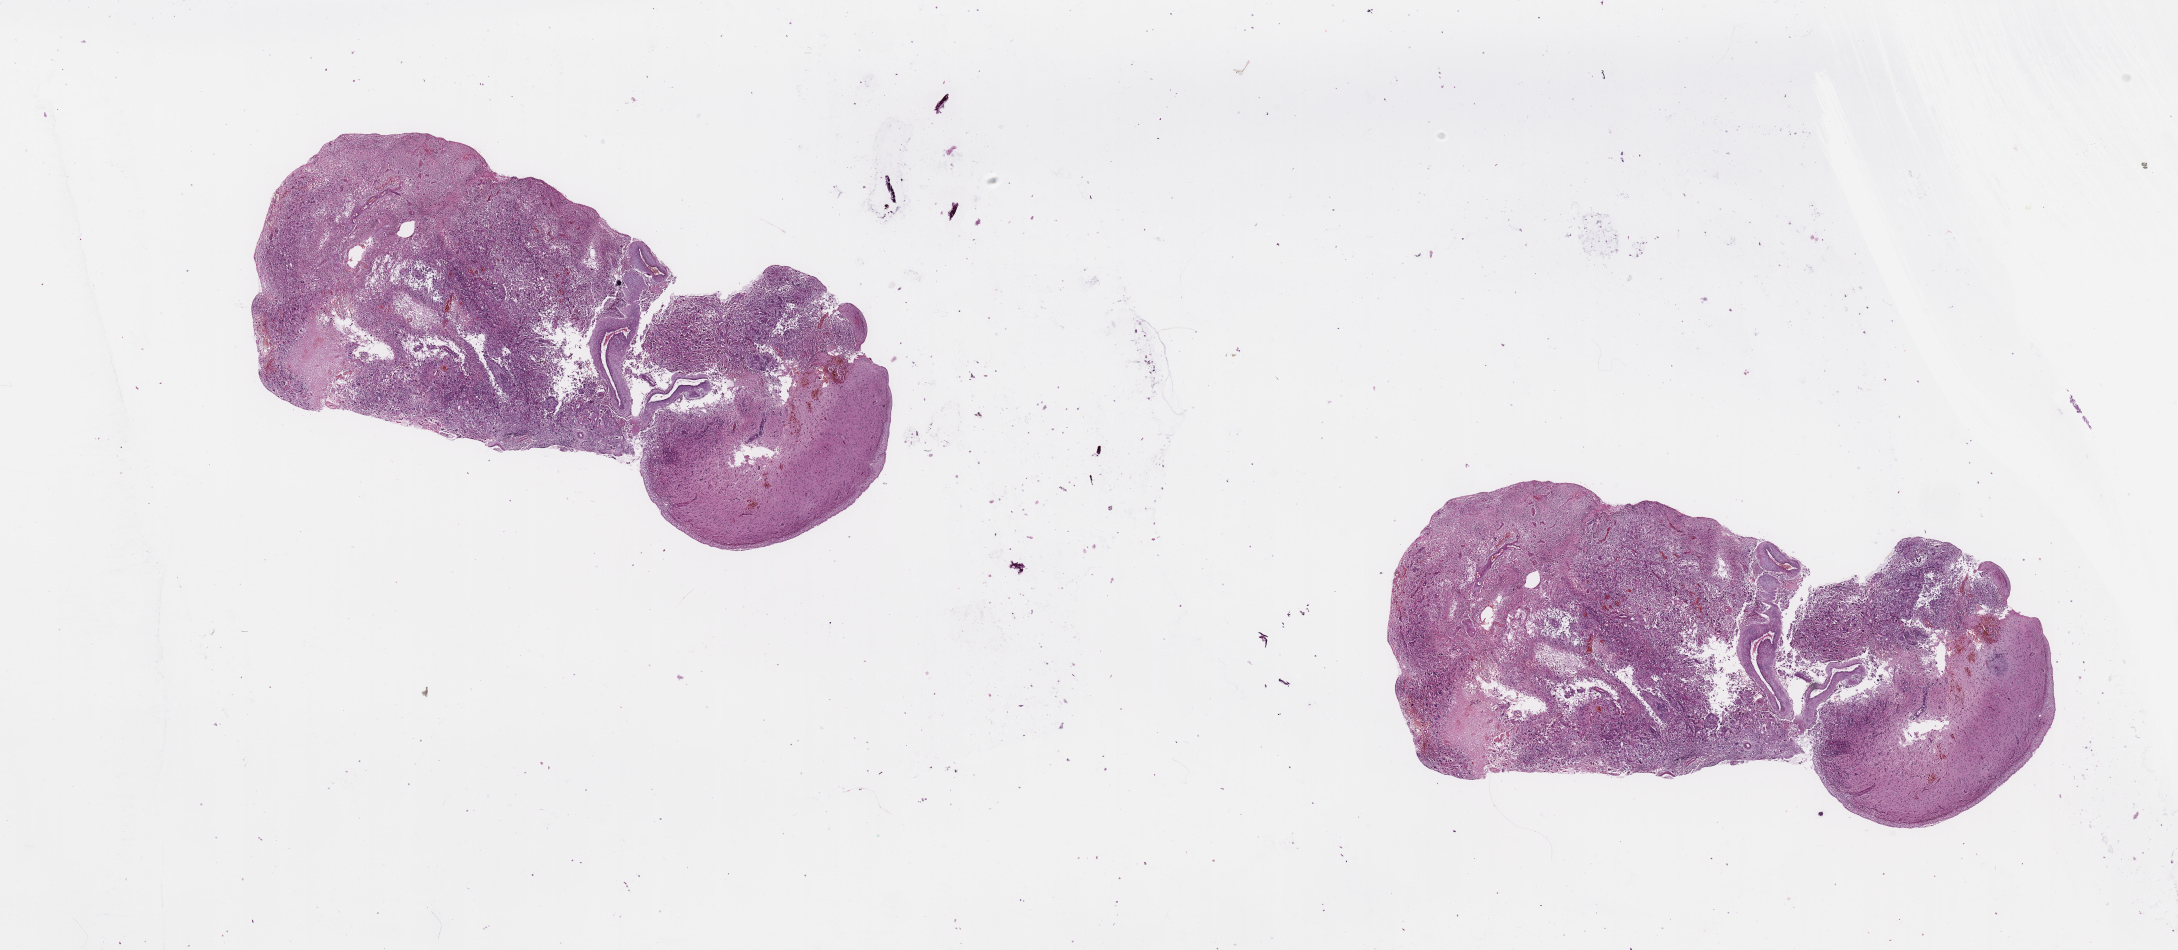
Digitized H&E-stained tissue section (whole slide) — a low-resolution overview of the entire scanned area, about 34.5 x 15.0 mm; brain, tumour tissue. Male, 77 y/o.
Histologic diagnosis: Glioblastoma. Primary tumour site (as recorded): frontal lobe.